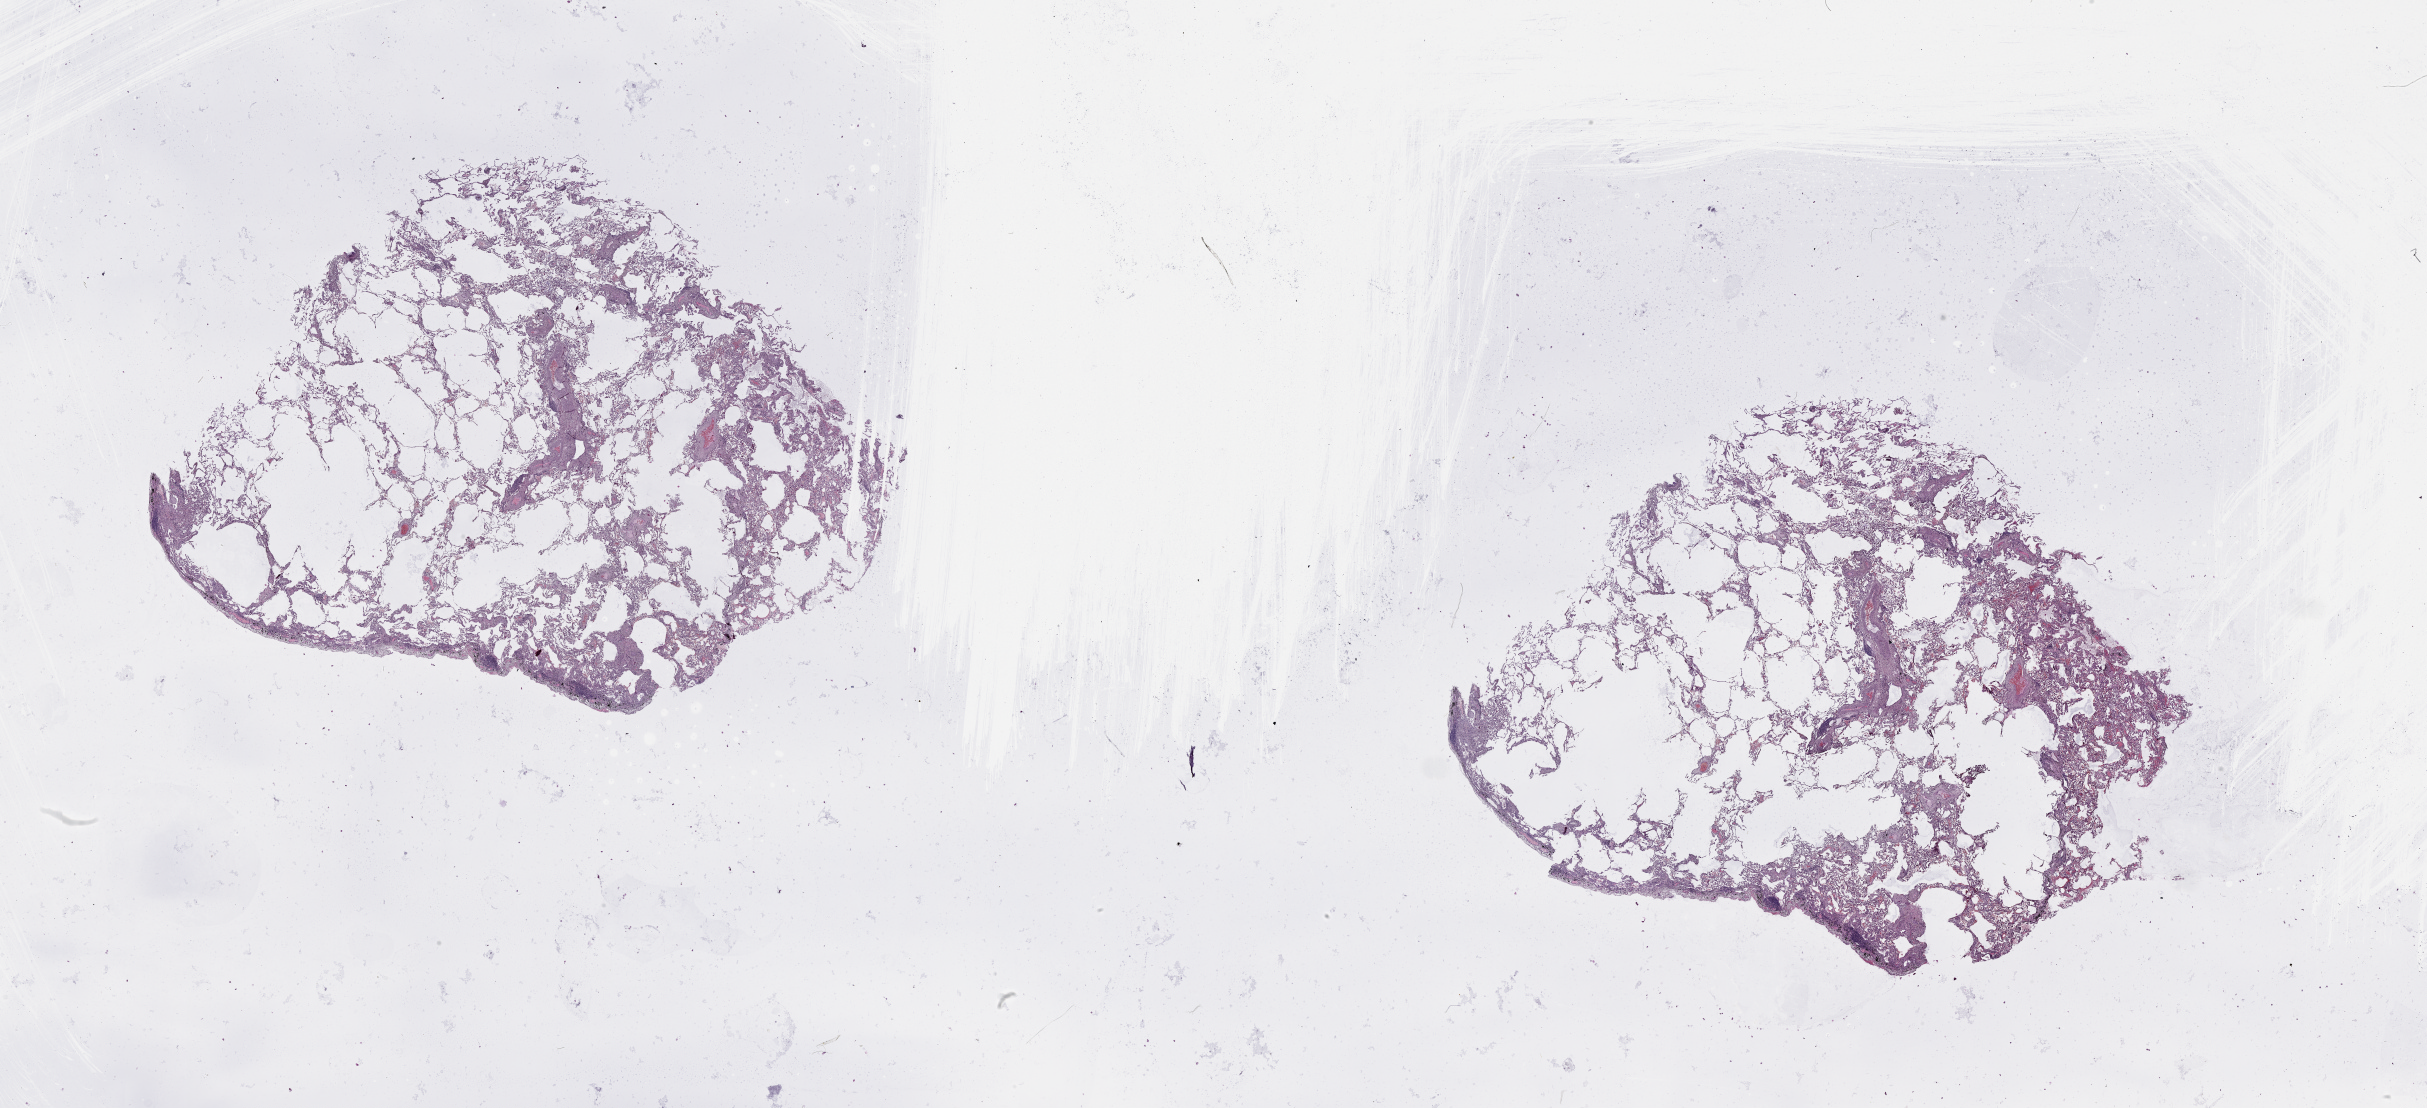
Digitized H&E-stained tissue section (whole slide) — whole scanned area (about 39.1 x 17.8 mm) shown as a low-resolution overview; normal (non-tumour) tissue sample, lung. 75-year-old male patient.
This section: normal (non-tumour) tissue from the same patient. Patient diagnosis (cohort enrolment): squamous cell carcinoma (lung).